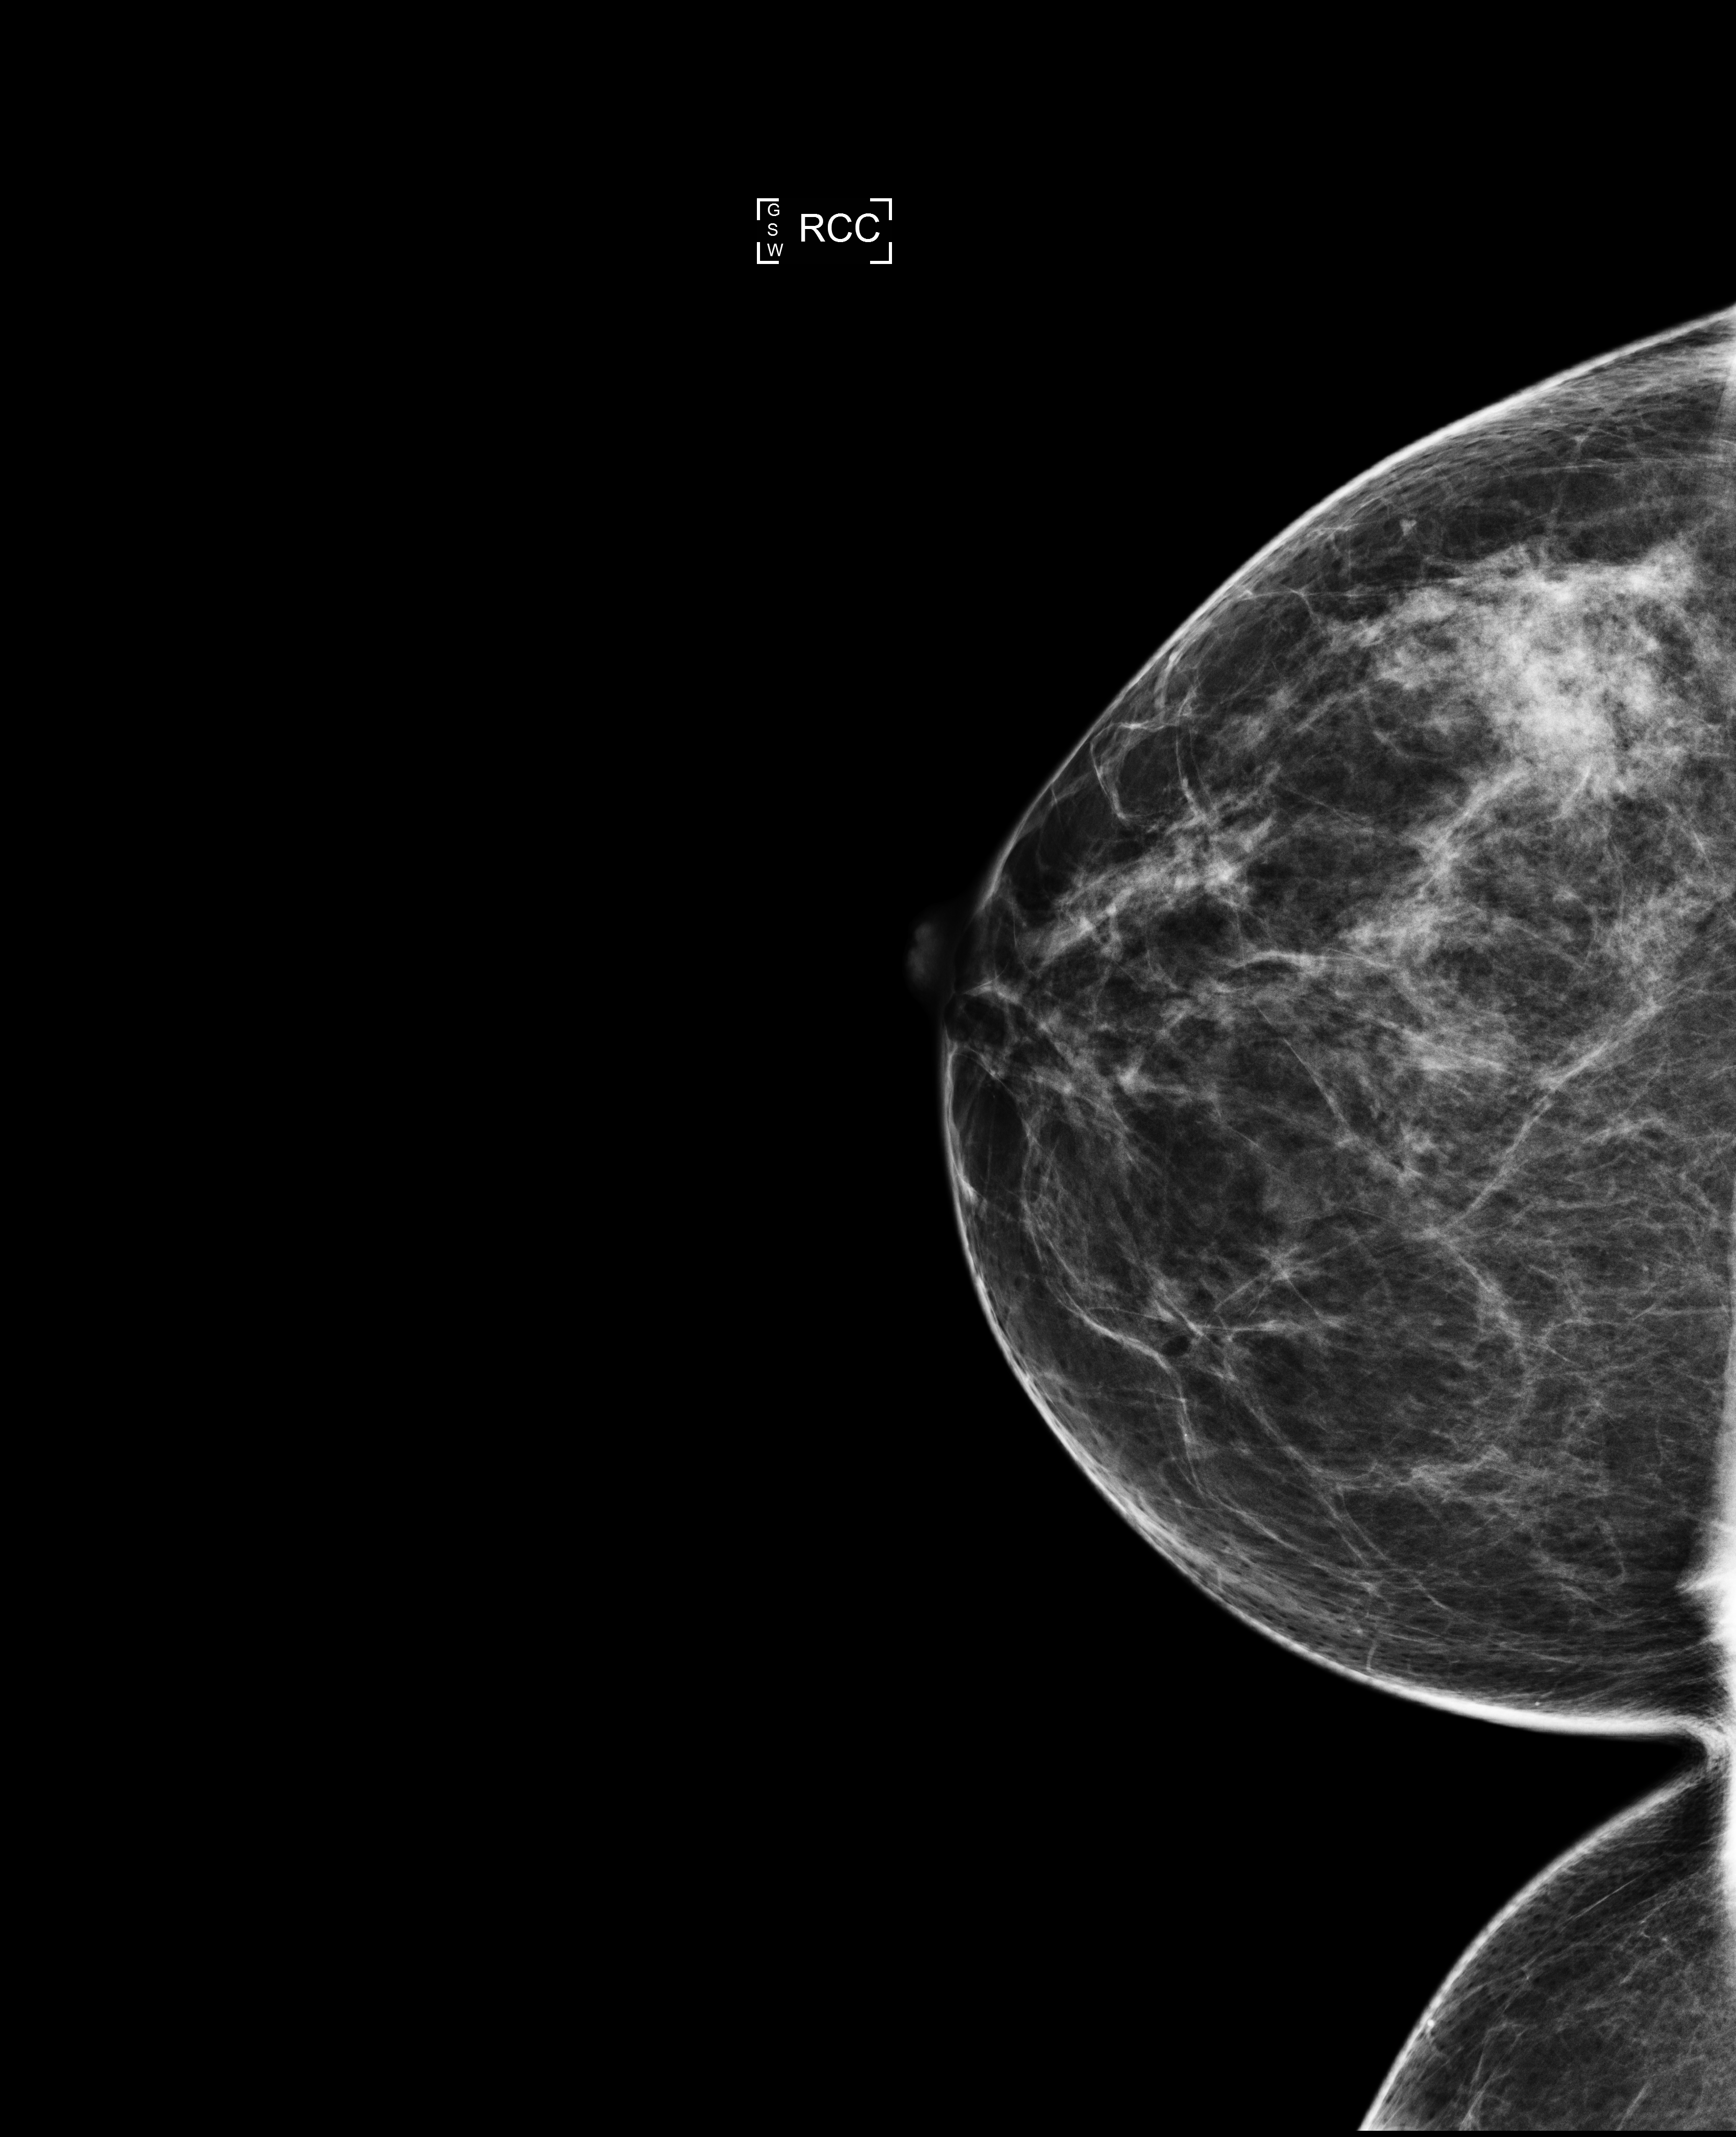
Full-field digital mammogram (FFDM); right breast; craniocaudal (CC) view; screening examination. Female patient, age 51 years.
- BI-RADS breast density category at the screening exam (both breasts, scale 1–4): 3
- final BI-RADS category for the screening round (tomosynthesis exam, both breasts): category 1
- recall: no recall after this screen